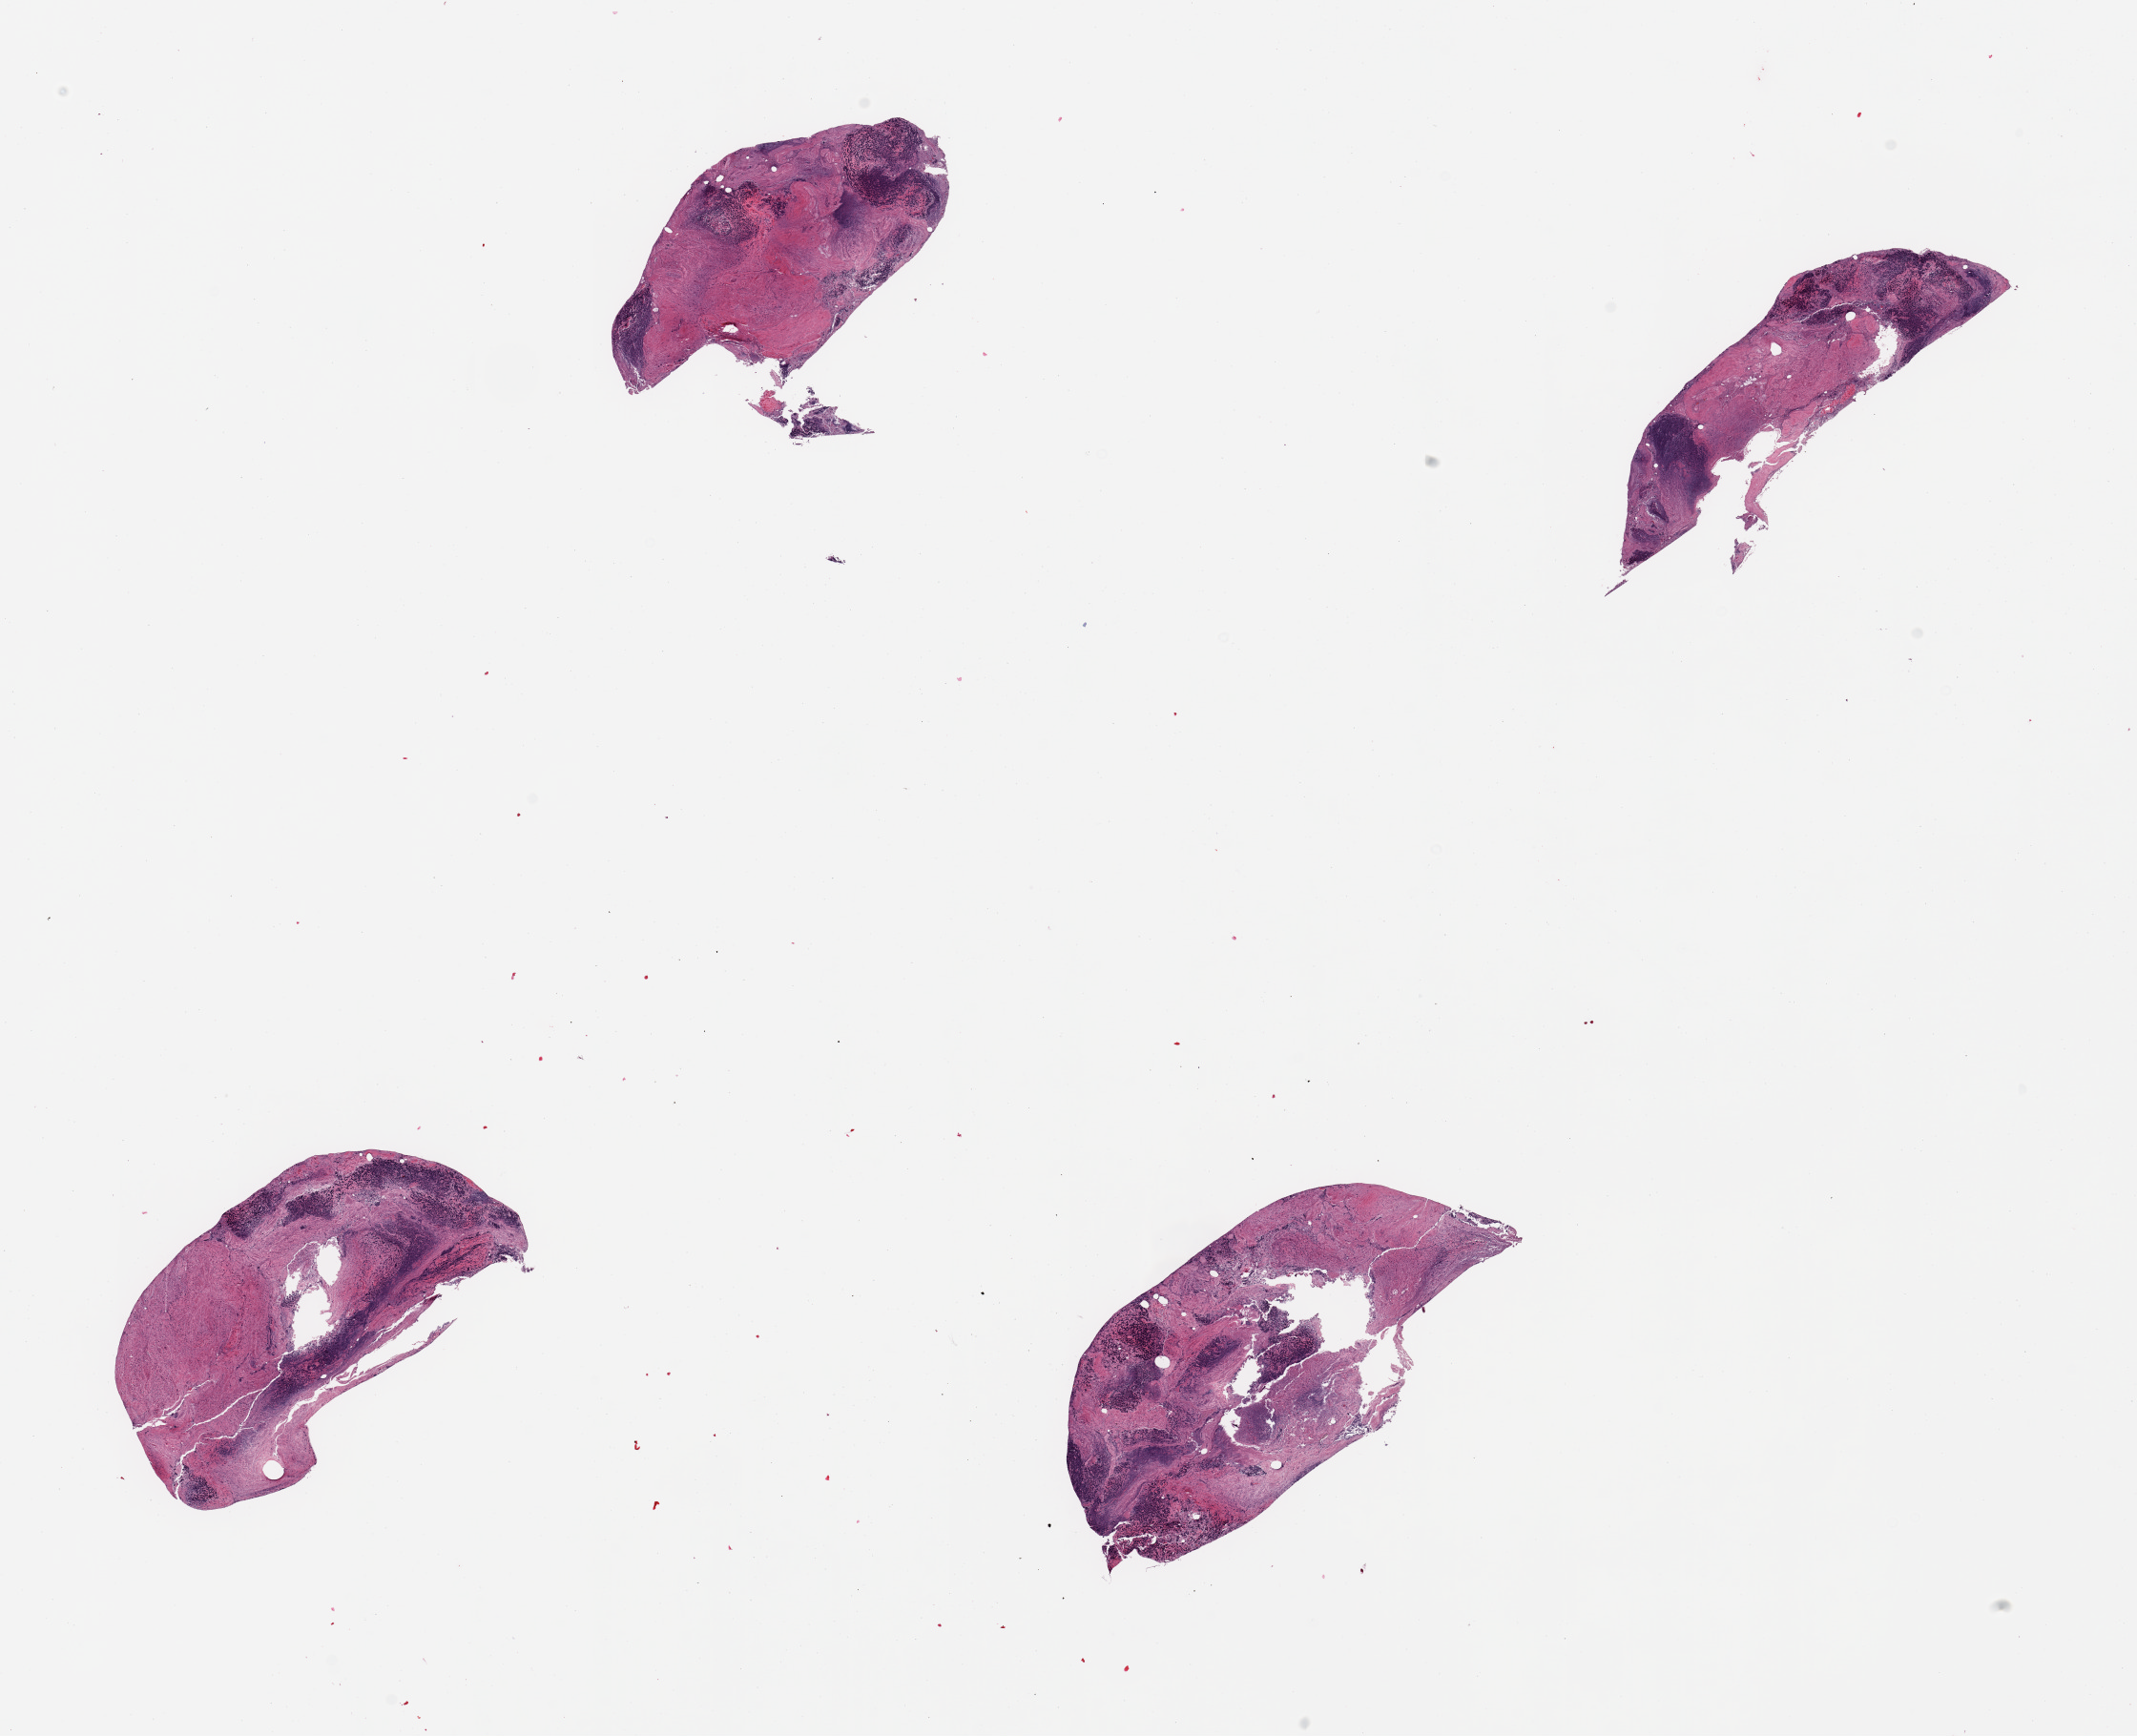
Haematoxylin and eosin whole-slide image — a low-resolution overview of the entire scanned area, about 17.7 x 14.4 mm (acquisition: 20x scan). PAXgene-fixed, paraffin-embedded tissue. Section of ileum (target tissue). Tissue donor sample.
Pathologist's review note for this sample: 4 pieces, mucosa autolyzed, ~30% residucal target lymphocytes.